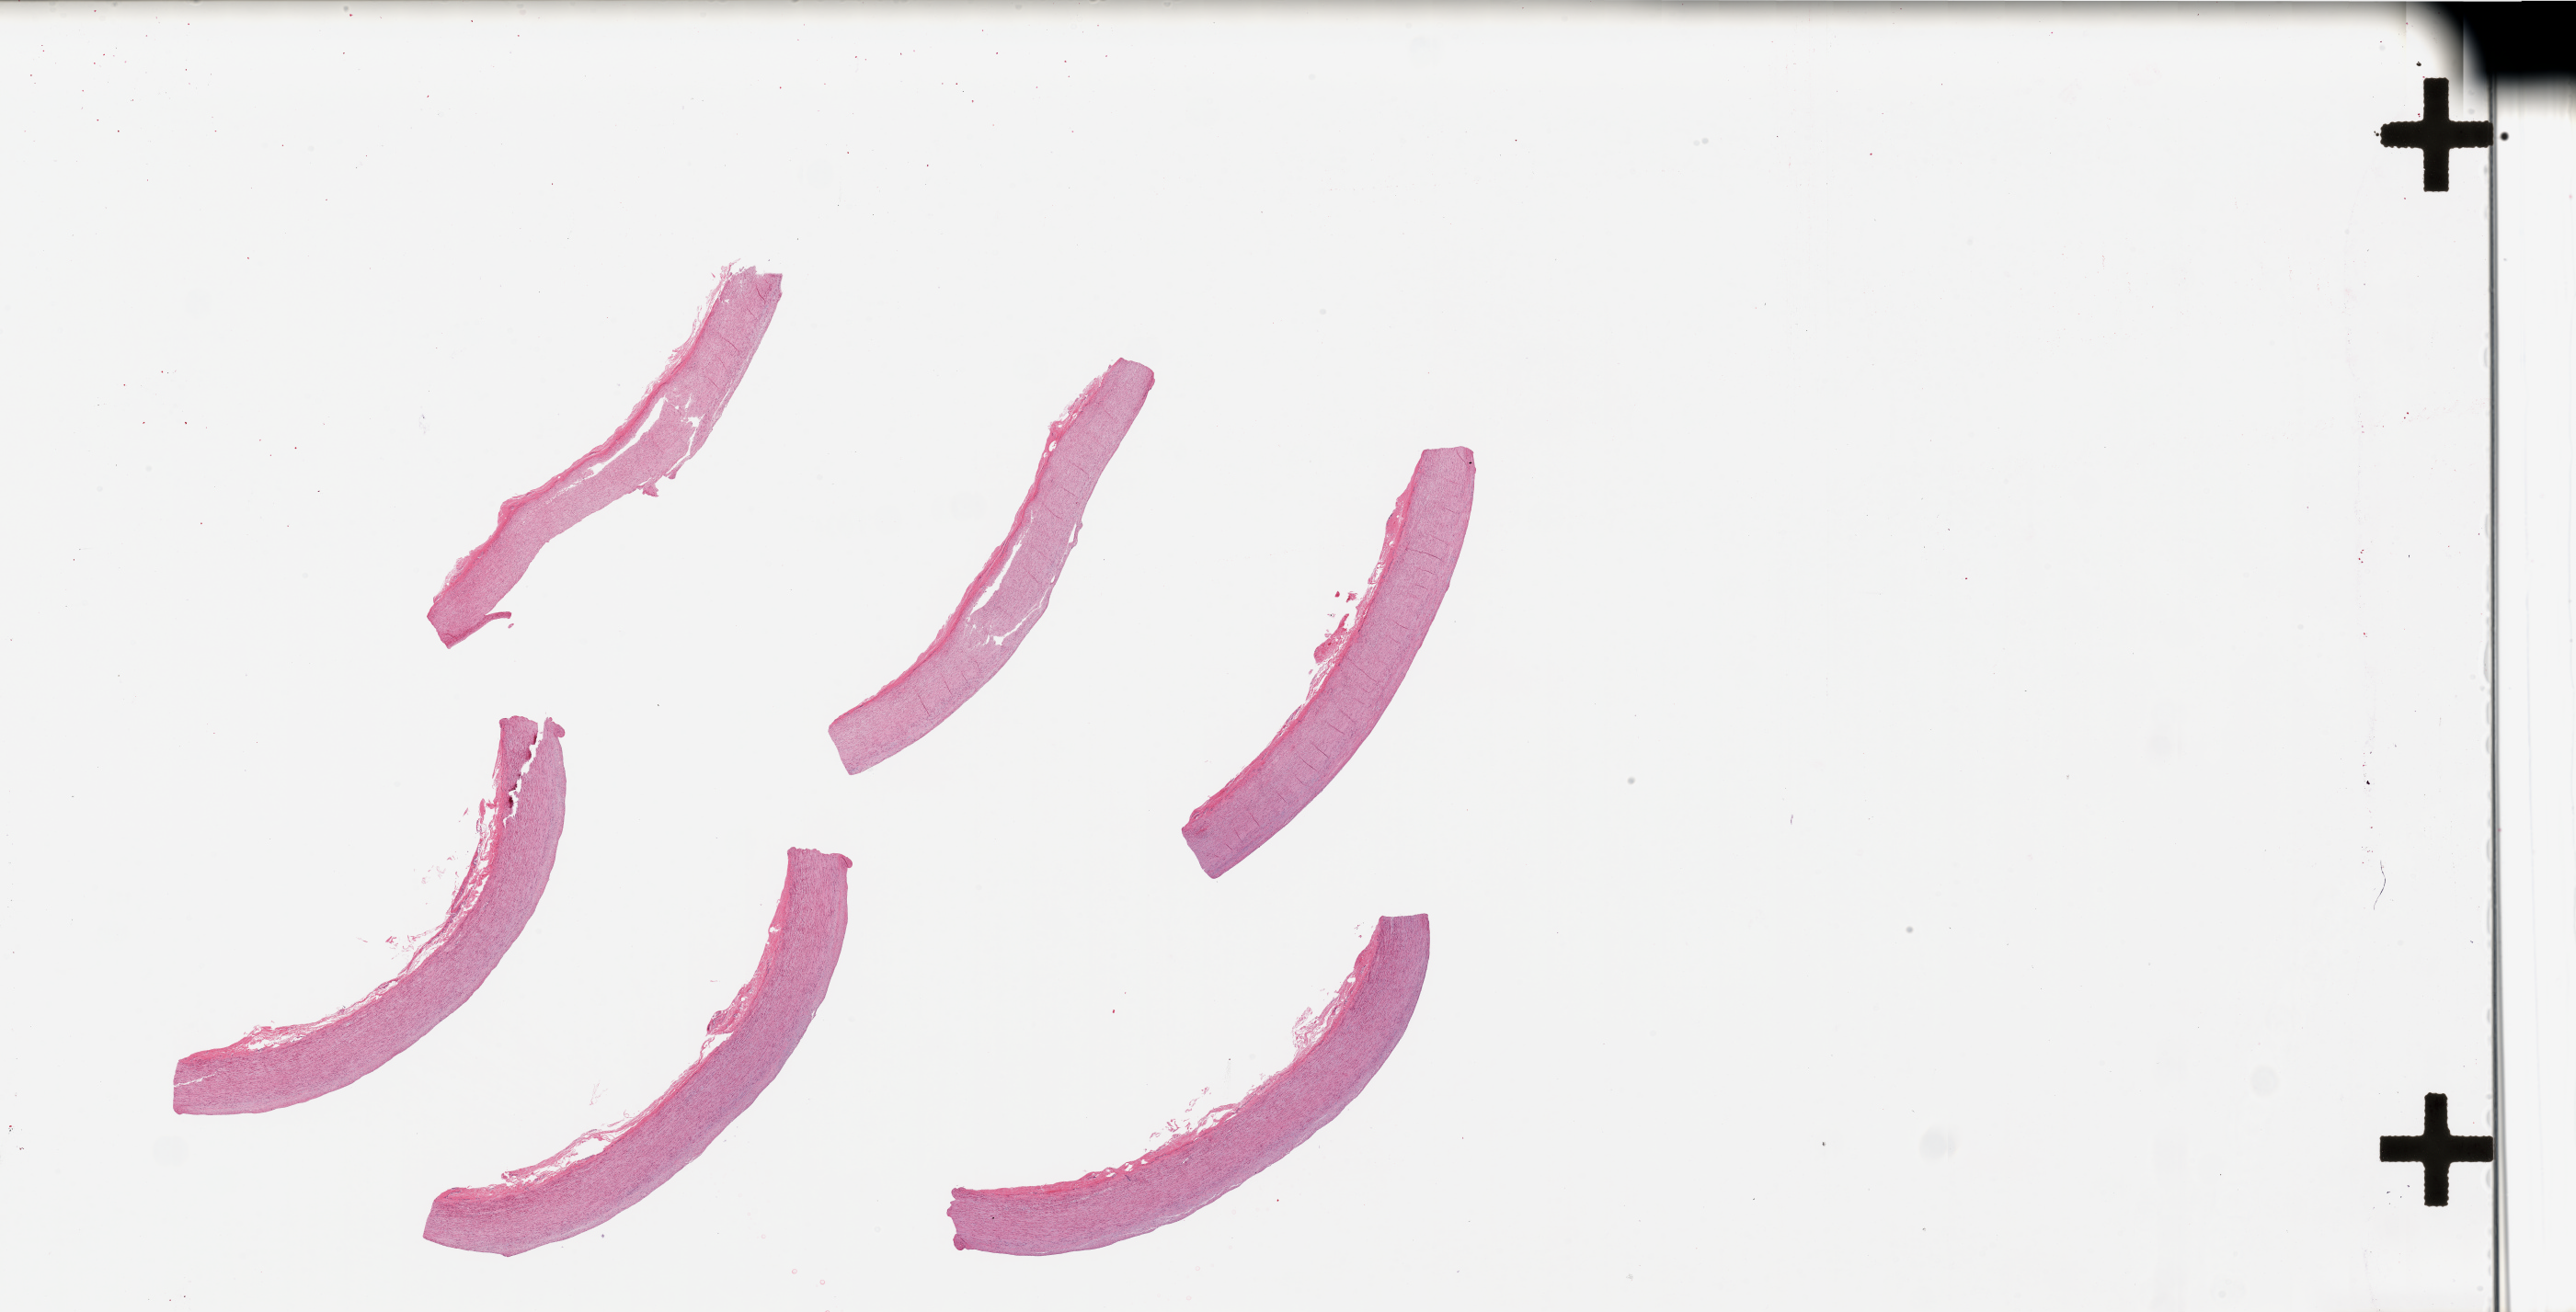
Whole-slide image, H&E stain, brightfield — shown as a low-resolution overview of the whole scanned area (about 44.3 x 22.6 mm); PAXgene-fixed paraffin-embedded (PFPE) section; section of aorta (target tissue); donor tissue sample. Donor sex: male.
Reviewer comment on this tissue sample: 6 pieces, up to 10x2mm; No plaques. No extraneous tissue.